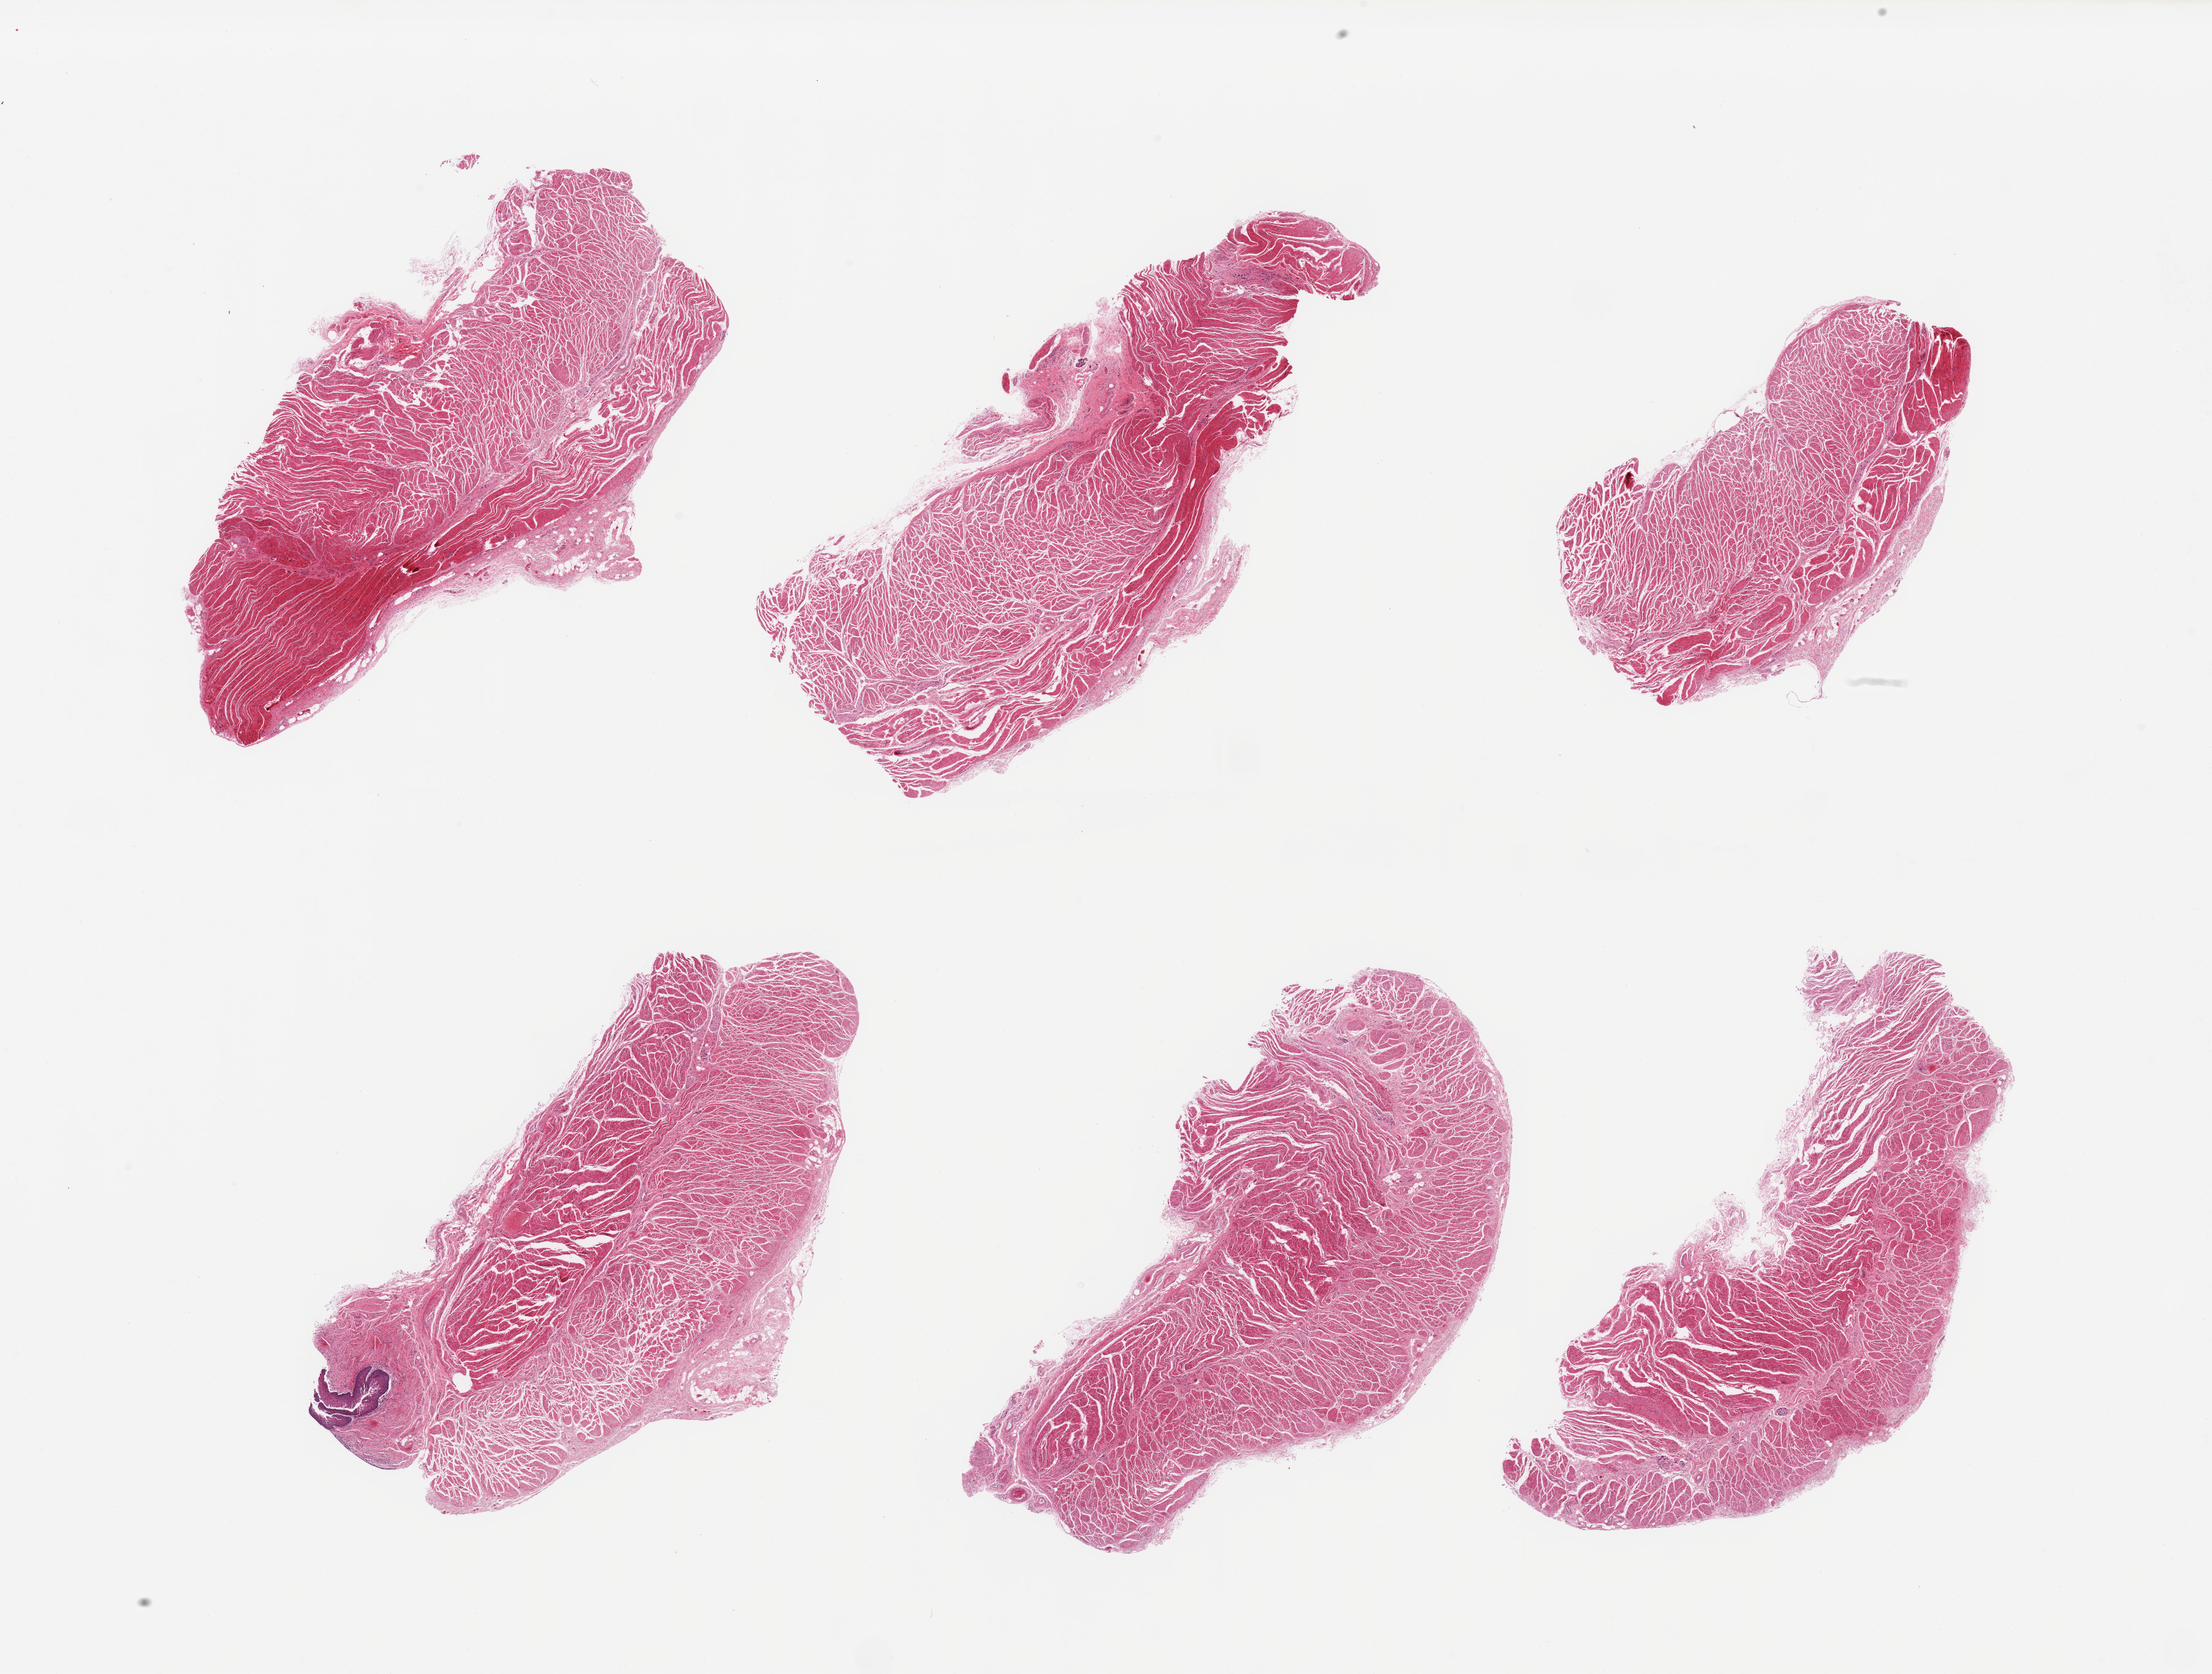
Whole-slide image, H&E stain — a low-resolution overview of the entire scanned area, about 28.5 x 21.6 mm (slide scanned at 20x), PAXgene-fixed paraffin-embedded (PFPE) section, section of gastroesophageal junction (target tissue), tissue donor sample. Donor sex: female.
* reviewer comment on this tissue sample: 6 pieces, confirmed target muscularis; trace contaminant squamous mucosa, <1mm nubbin